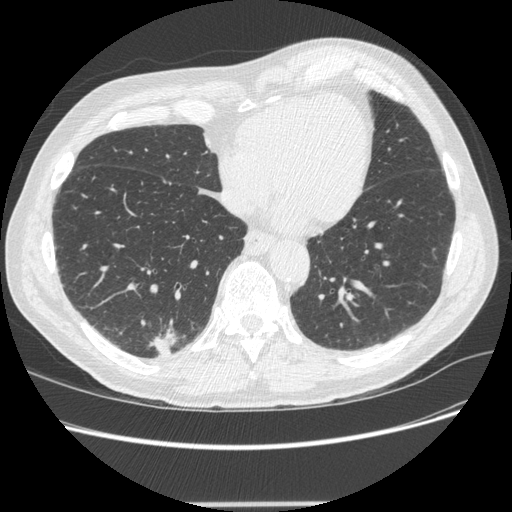
Low-dose screening chest CT, one axial slice; slice 75 of 245 in the series (ordered by position); reconstruction kernel STANDARD; 120 kVp; lung window (W 1500 / L -600 HU); 1.25 mm slice thickness; 512 × 512 image matrix.
Annotated regions visible in this slice (outlined manually by an expert reader):
- lesion 1 (tumor, lower lobe of right lung): bounding box <150,327,179,356> (left, top, right, bottom; pixels)